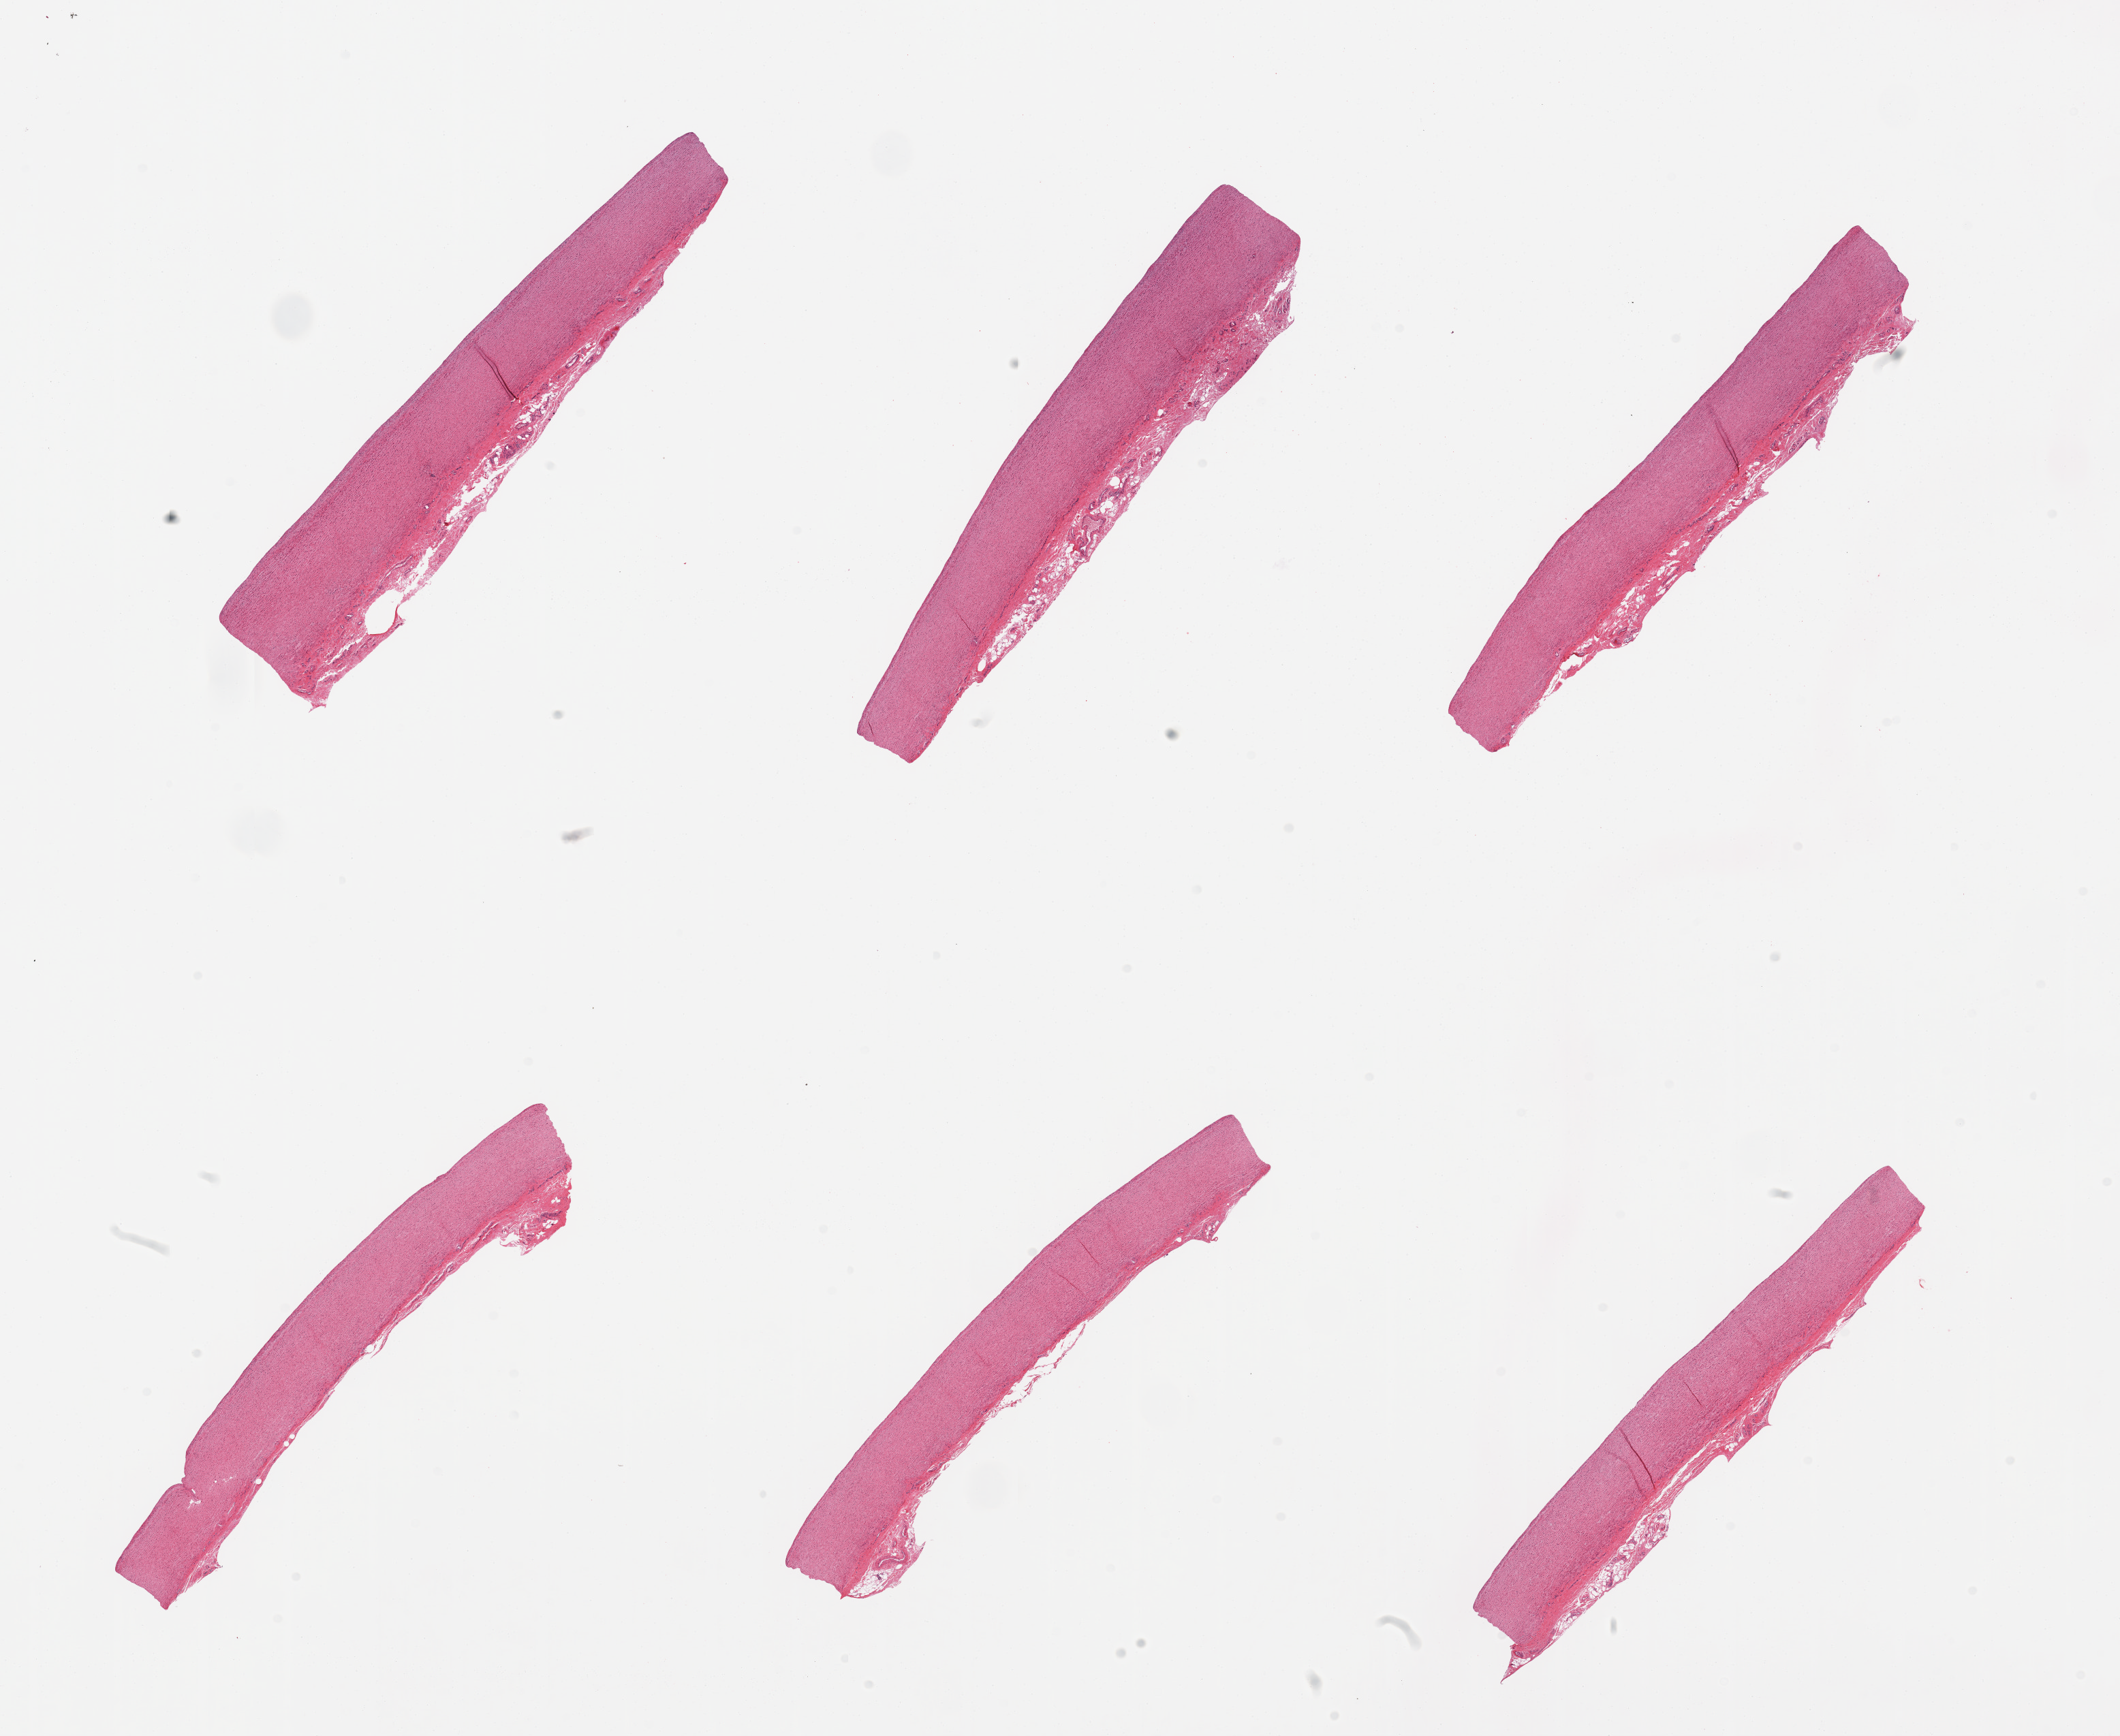
Whole-slide image, hematoxylin and eosin (H&E) stain, a low-resolution overview of the entire scanned area, about 24.6 x 20.2 mm (slide scanned at 20x). PAXgene-fixed, paraffin-embedded tissue. Section of aorta (target tissue). Donor tissue sample. Donor: male.
Pathologist's review note for this sample: 6 pieces.